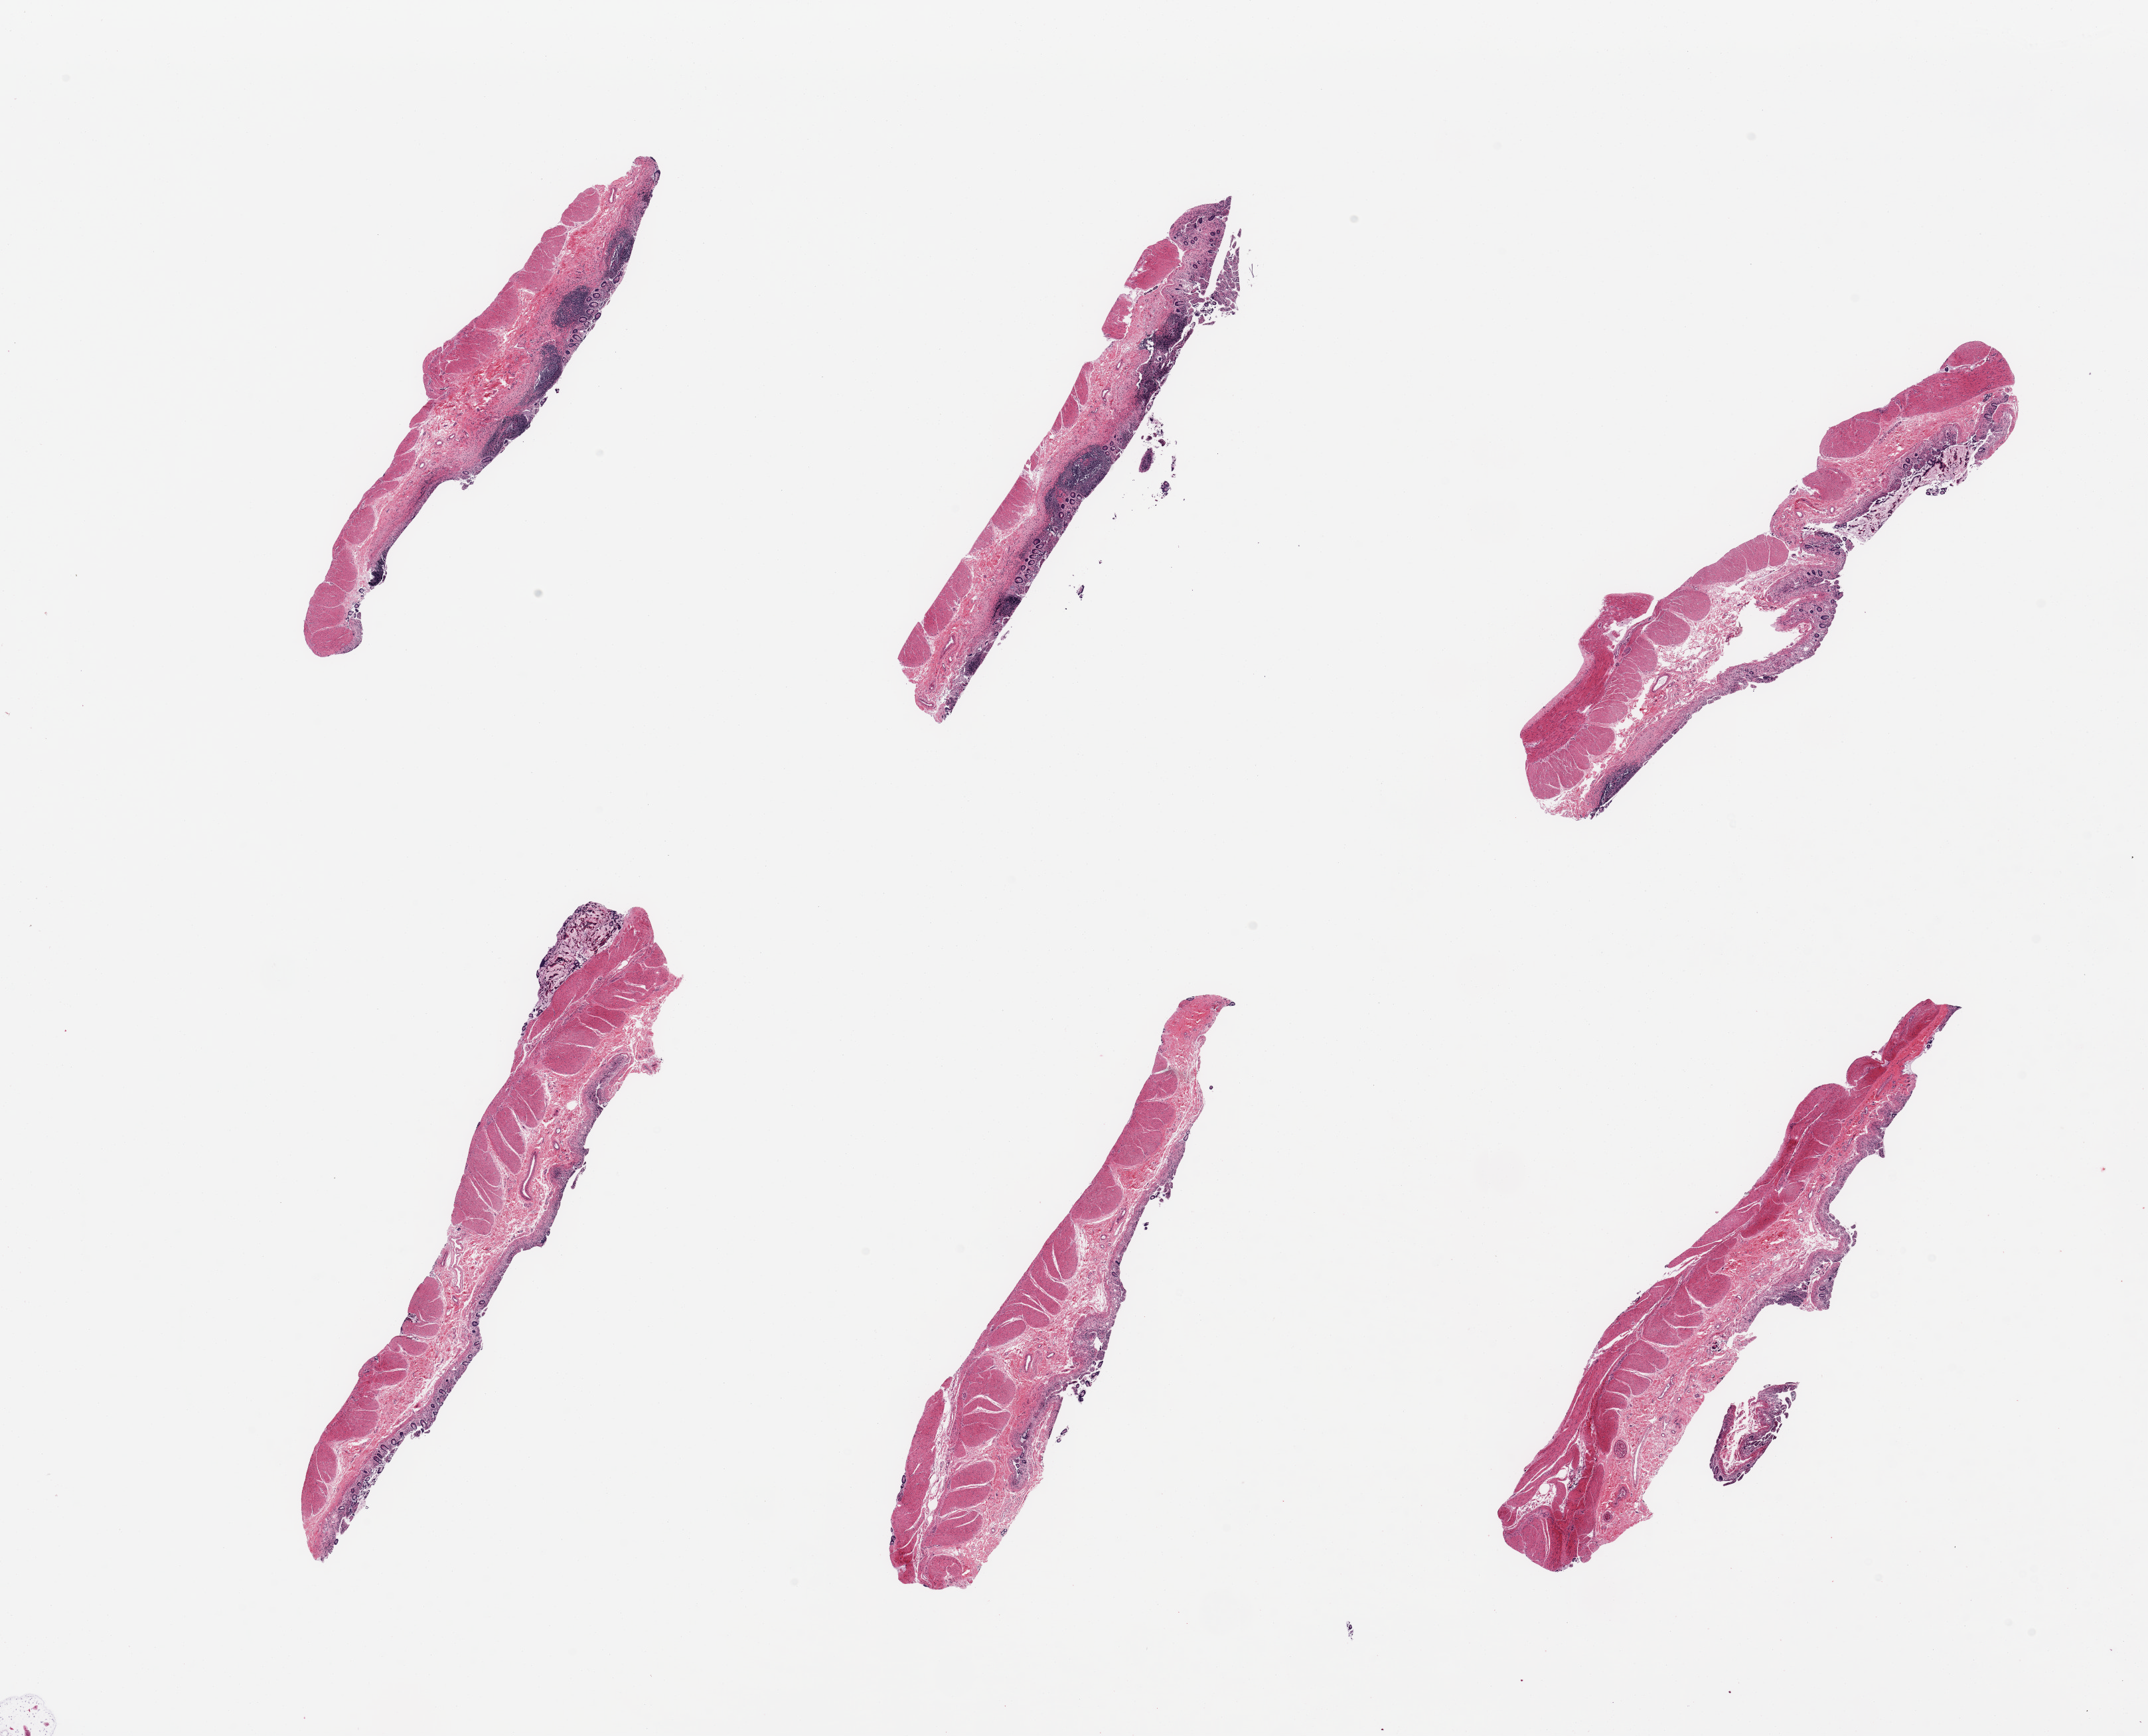
Whole-slide image, haematoxylin and eosin stain, brightfield — low-resolution overview of the scanned area, about 25.6 x 20.7 mm (from a 20x scan); PAXgene-fixed paraffin-embedded (PFPE) section; sampled site (target tissue): ileum; donor tissue sample.
Pathologist's review note for this sample: 6 pieces; autolyzed mucosa; ~ 15% tissue is residual target lymphoid aggregates, all include muscularis (not target).